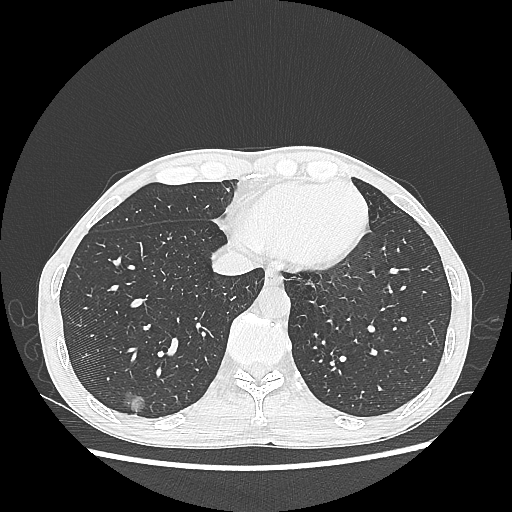
Chest CT, one axial slice. Lung window (W 1500 / L -600 HU). 1.25 mm slice thickness. 512 × 512 image matrix, field of view 360 × 360 mm. Patient: male, 60 years. From the clinical record (not read from this slice): clinical TNM (as recorded): T1c N0 M0; histopathological grade: G2.
Structures marked on this image (rectangle marked by the reading radiologist):
- lung tumour (recorded histology: adenocarcinoma): box from (x=122, y=386) to (x=147, y=417) px